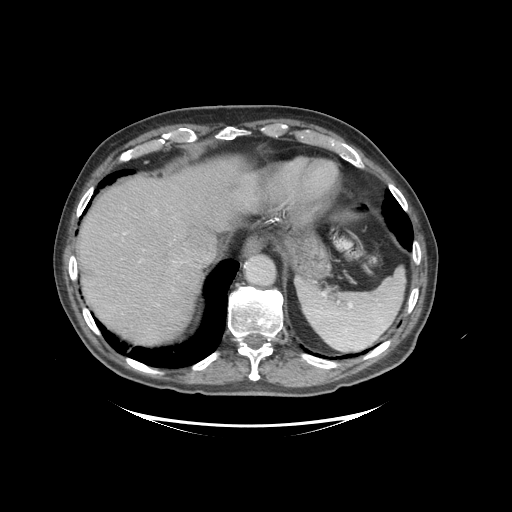
Contrast-enhanced abdominal CT (liver protocol), one axial slice. Slice 80 of 99 in the series (ordered by position). Reconstruction kernel STANDARD. 140 kVp. Soft-tissue window (W 400 / L 40 HU). 2.5 mm slice thickness. 512 × 512 image matrix. Case-level facts recorded for this patient, not image findings: diagnosis: hepatocellular carcinoma (patient treated with transarterial chemoembolisation; whether this scan precedes or follows treatment is not stated here); TNM stage (as recorded): Stage-I; Child-Pugh class: A.
Annotated regions visible in this slice (semi-automatic segmentation, software-assisted and operator-edited):
- liver parenchyma outside the tumour (the mass and vessels are separate outlines, so this box may not span the whole liver): bounding box <78,158,262,344> (left, top, right, bottom; pixels)
- liver vessels: <124,232,126,235>